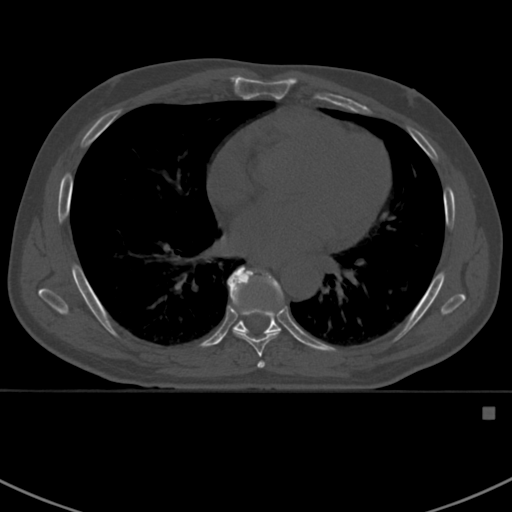
CT including the spine, one axial slice. Slice 410 of 412 in the series (ordered by position). Reconstruction kernel Br40s. Bone window (W 1800 / L 400 HU). 1.5 mm slice thickness. 512 × 512 image matrix. Patient: male, 59 years. Case-level facts recorded for this patient, not image findings: primary cancer: prostate.
Annotated regions visible in this slice (semi-automatic segmentation, software-assisted and operator-edited):
- T7 vertebra: bounding box [x1, y1, x2, y2] px = [228, 280, 284, 368]
- T8 vertebra: [227, 266, 284, 336]